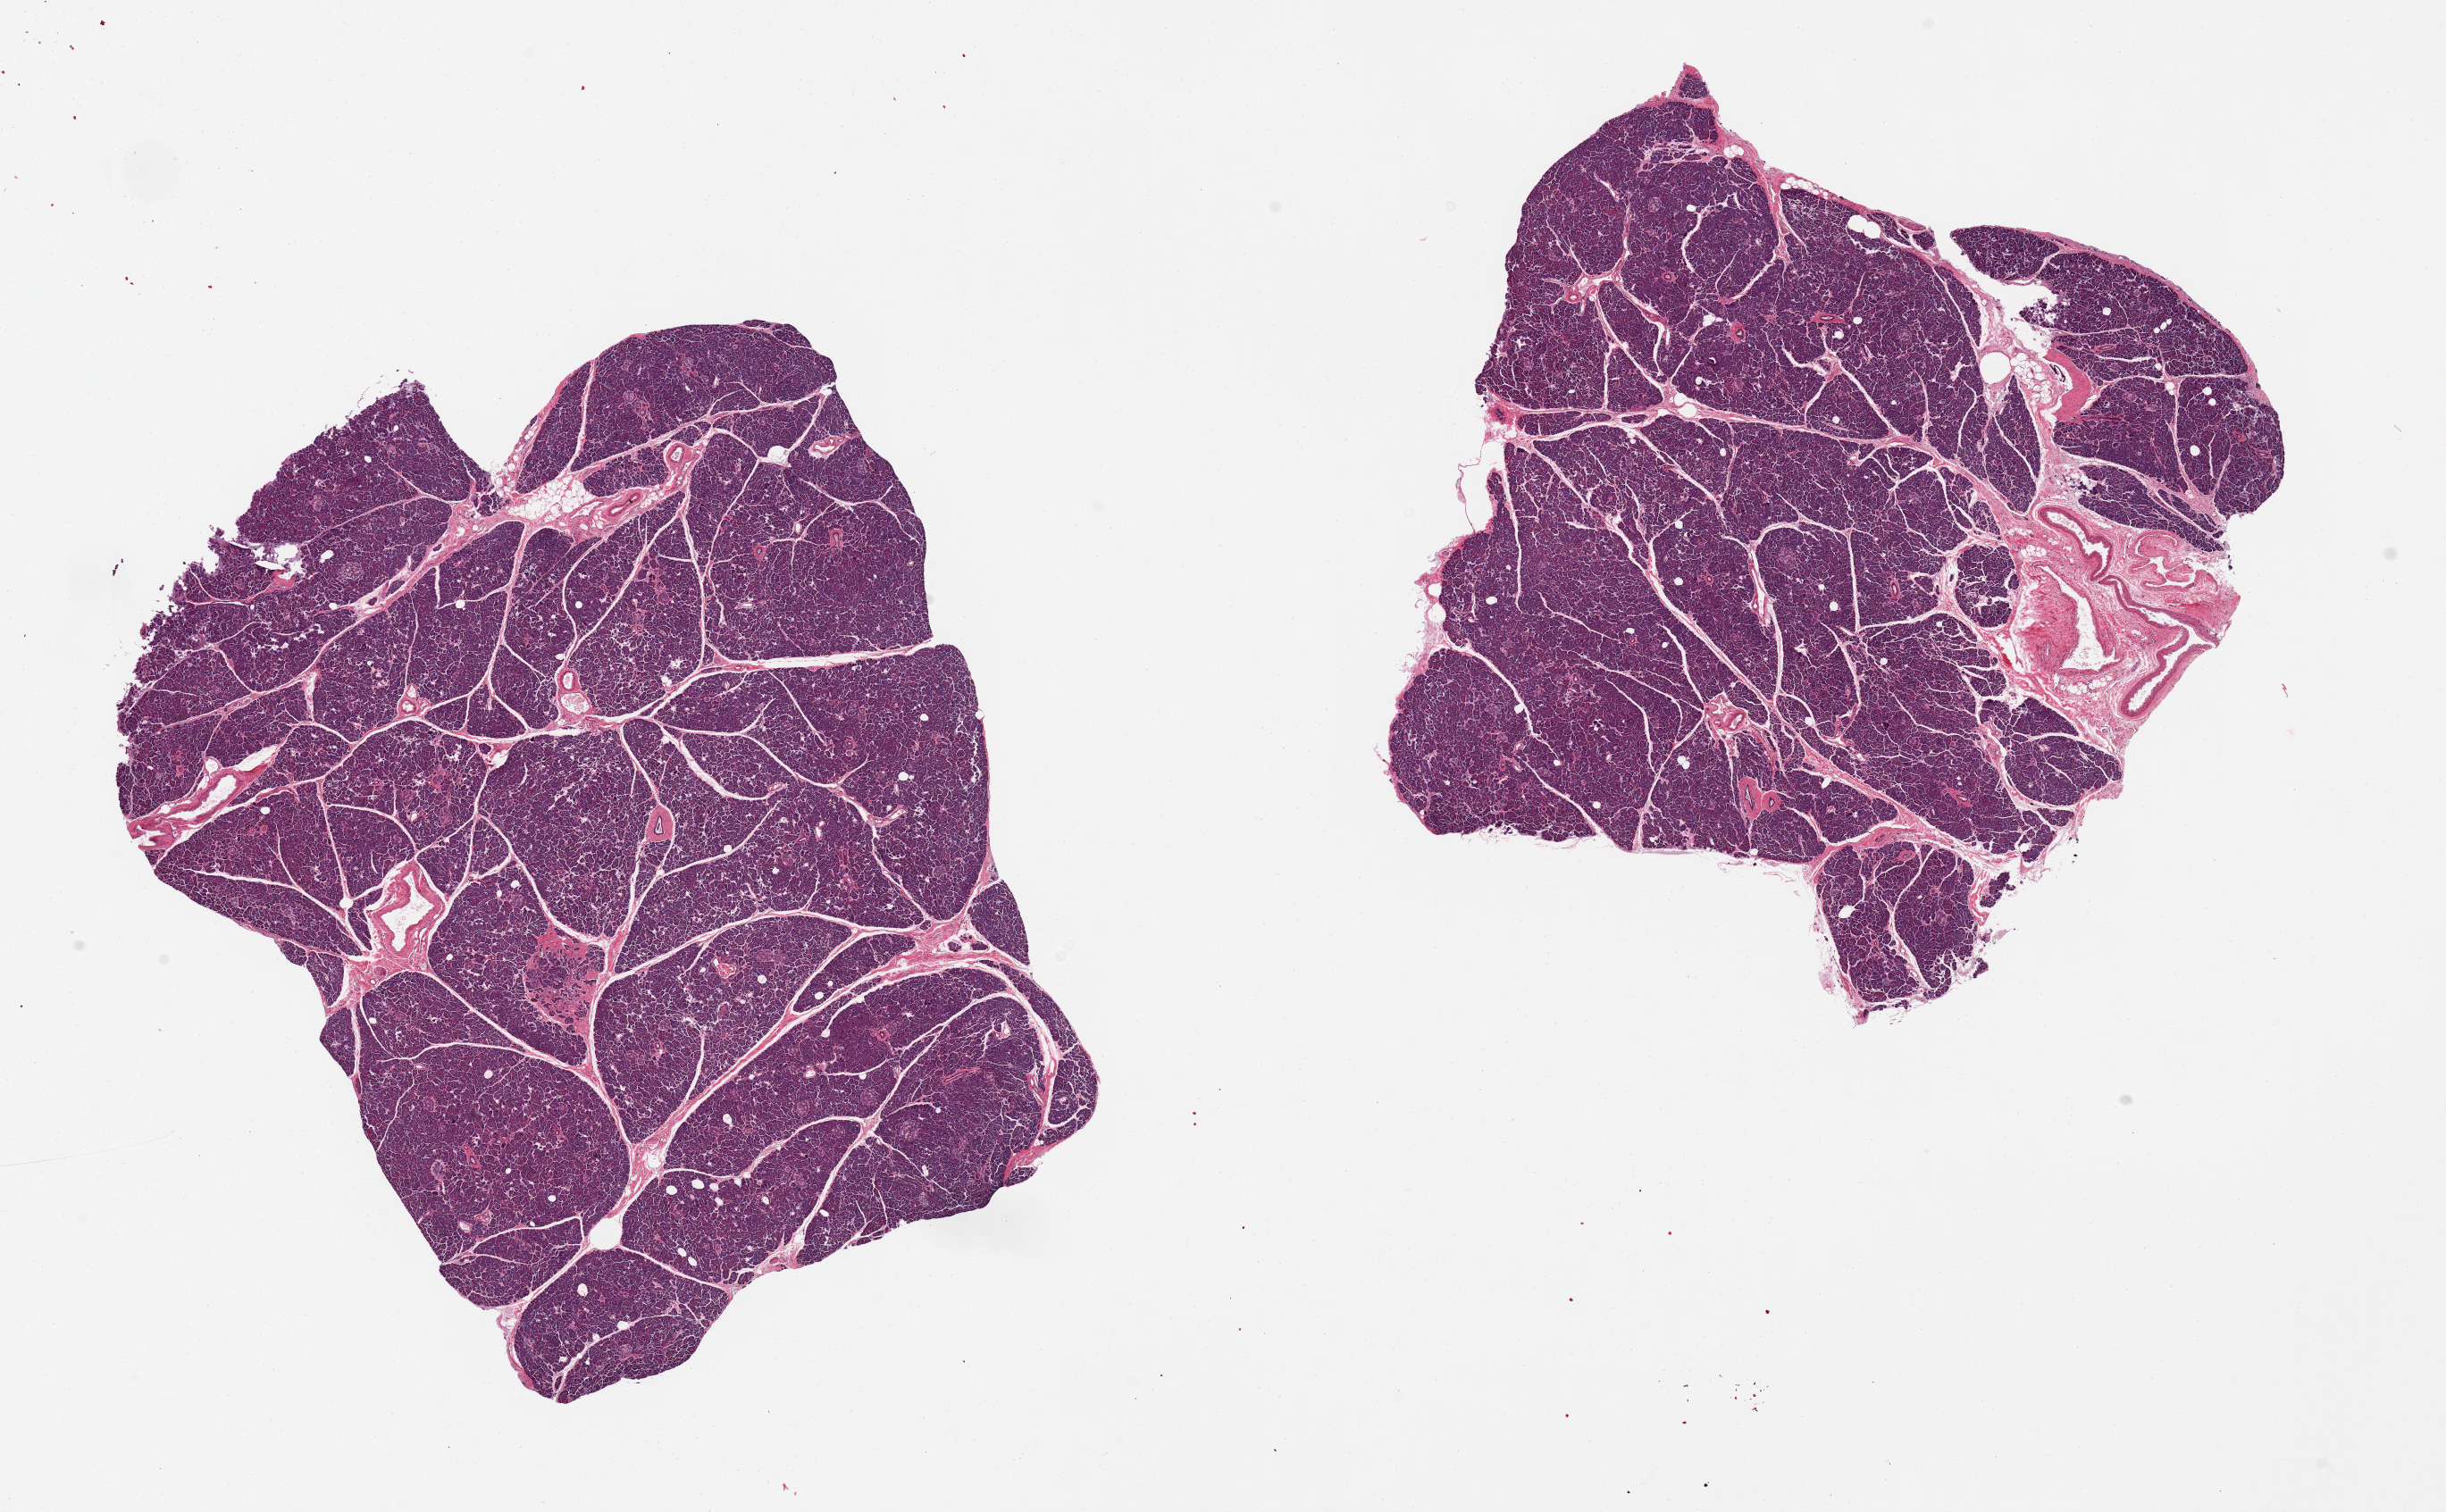
Haematoxylin and eosin whole-slide image, shown as a low-resolution overview of the whole scanned area (about 21.7 x 13.4 mm). PAXgene-fixed, paraffin-embedded tissue. Section of pancreas (target tissue). Donor tissue sample. Donor sex: female.
Pathologist's review note for this sample: 2 pieces. 9x8 & 7x7mm; Very well dissected. no extraneous adipose. 2mm focus of blood vessels.